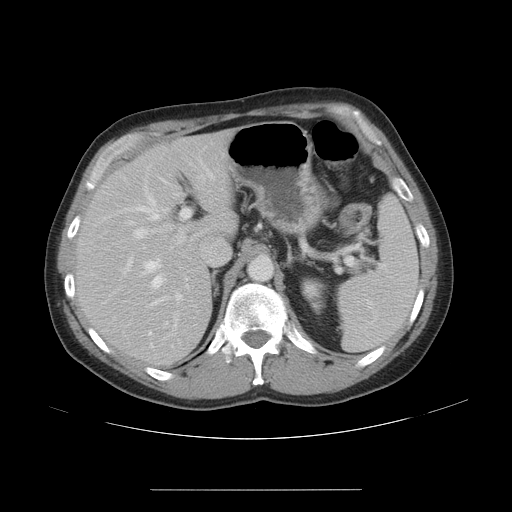
Contrast-enhanced abdominal CT, one axial slice; position 31 of 48 along the scan axis; reconstruction kernel STANDARD; intravenous contrast given; soft-tissue window (W 400 / L 40 HU); 5 mm slice thickness; 512 × 512 image matrix, field of view 409 × 409 mm. Male patient, age 56 years. From the clinical record (not read from this slice): diagnosis: colorectal cancer liver metastases, imaged before liver resection; multiple liver metastases: yes; largest metastasis: 1.8 cm; chemotherapy before resection: yes.
Annotated regions visible in this slice (expert manual segmentation):
- hepatic veins: box from (x=98, y=179) to (x=169, y=336) px
- liver: (x=77, y=133)–(x=233, y=365)
- planned liver remnant (the part of the liver to remain after resection): (x=78, y=133)–(x=233, y=365)
- portal vein (with intrahepatic branches): (x=103, y=159)–(x=216, y=306)